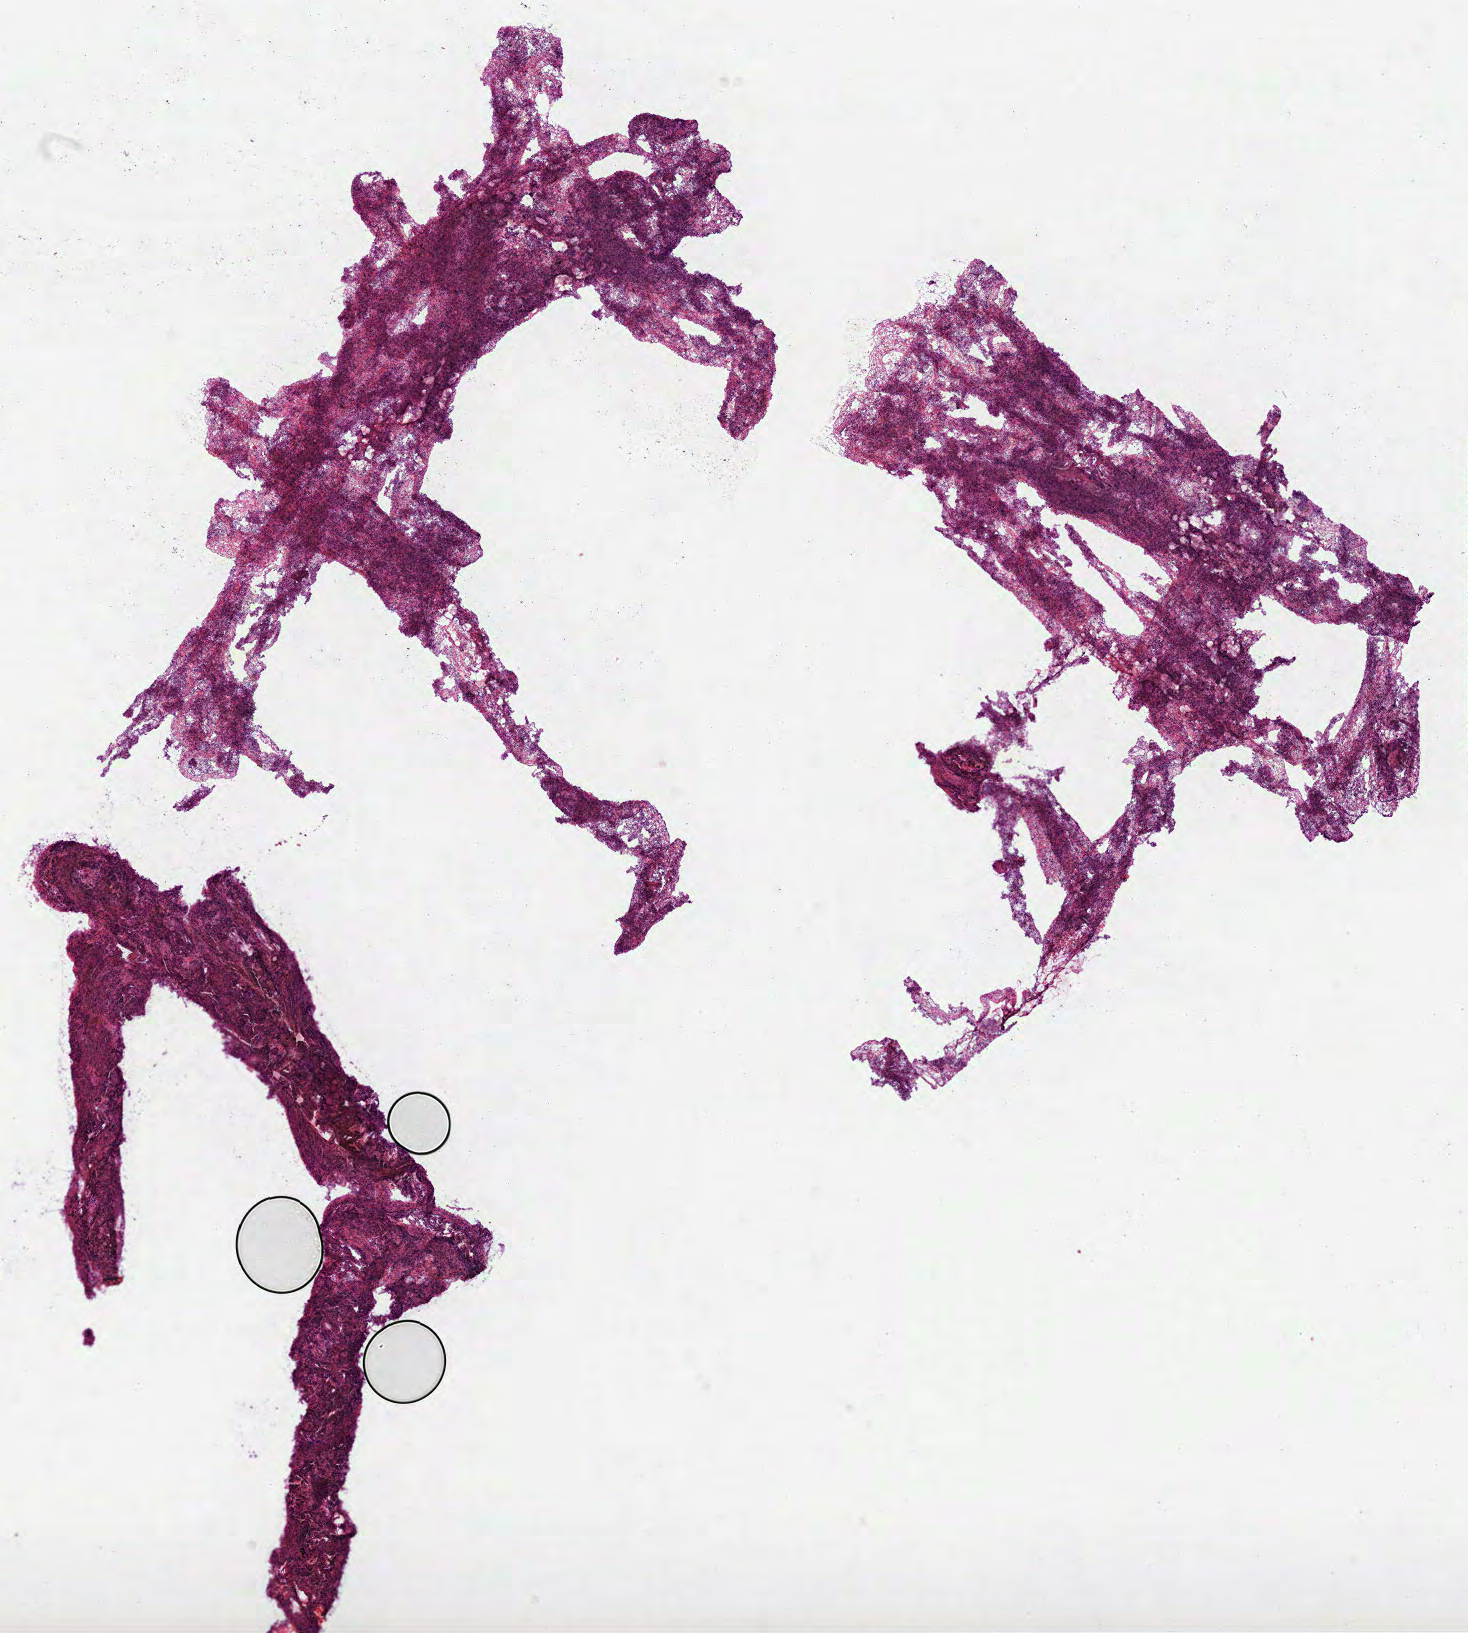
H&E whole-slide image, shown as a low-resolution overview of the whole scanned area (about 11.8 x 13.2 mm); frozen section from the top of the tissue portion; lung, solid tissue normal (non-tumour tissue) sample. Female patient; age at initial diagnosis 77 years.
This section: solid tissue normal sample (biorepository sample class). Patient diagnosis: Mucinous adenocarcinoma.